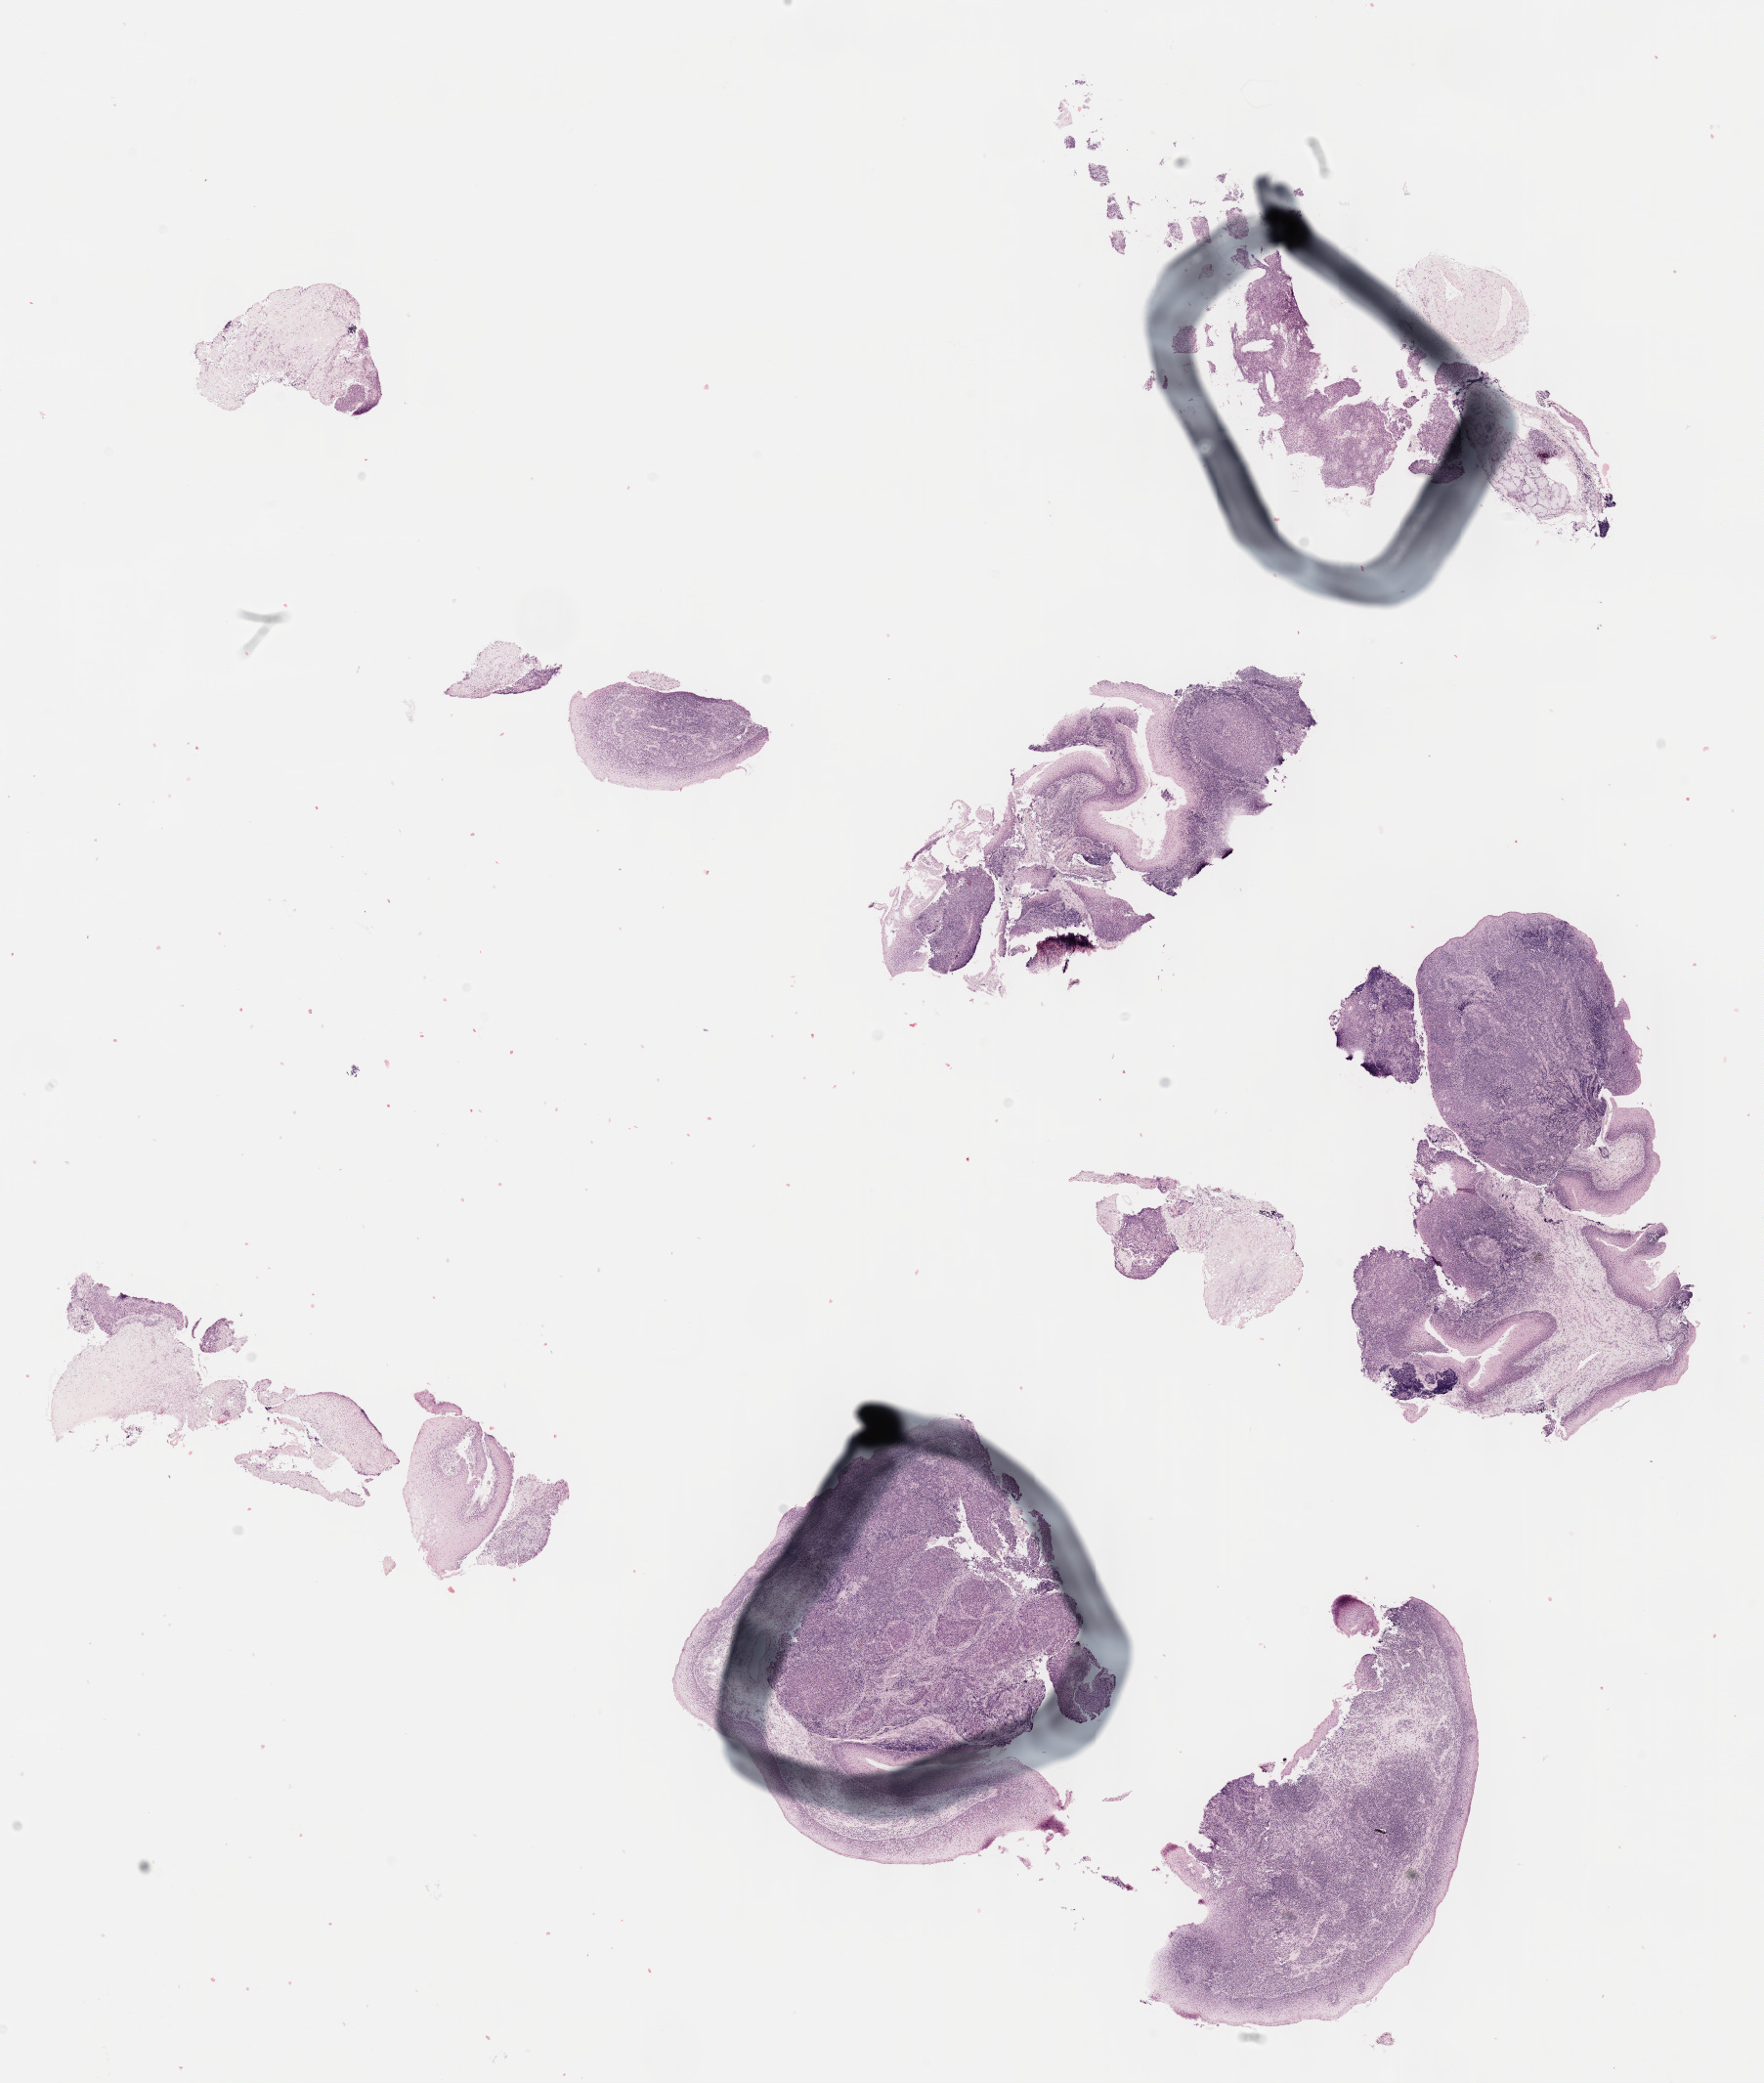
Whole-slide histology image, H&E-stained — shown as a low-resolution overview of the whole scanned area (about 14.6 x 17.2 mm), formalin-fixed paraffin-embedded (FFPE) diagnostic section, sample: primary tumour, head and neck. Male, age 51 years at initial diagnosis.
Pathologic diagnosis: Squamous cell carcinoma, NOS (tonsil, NOS).